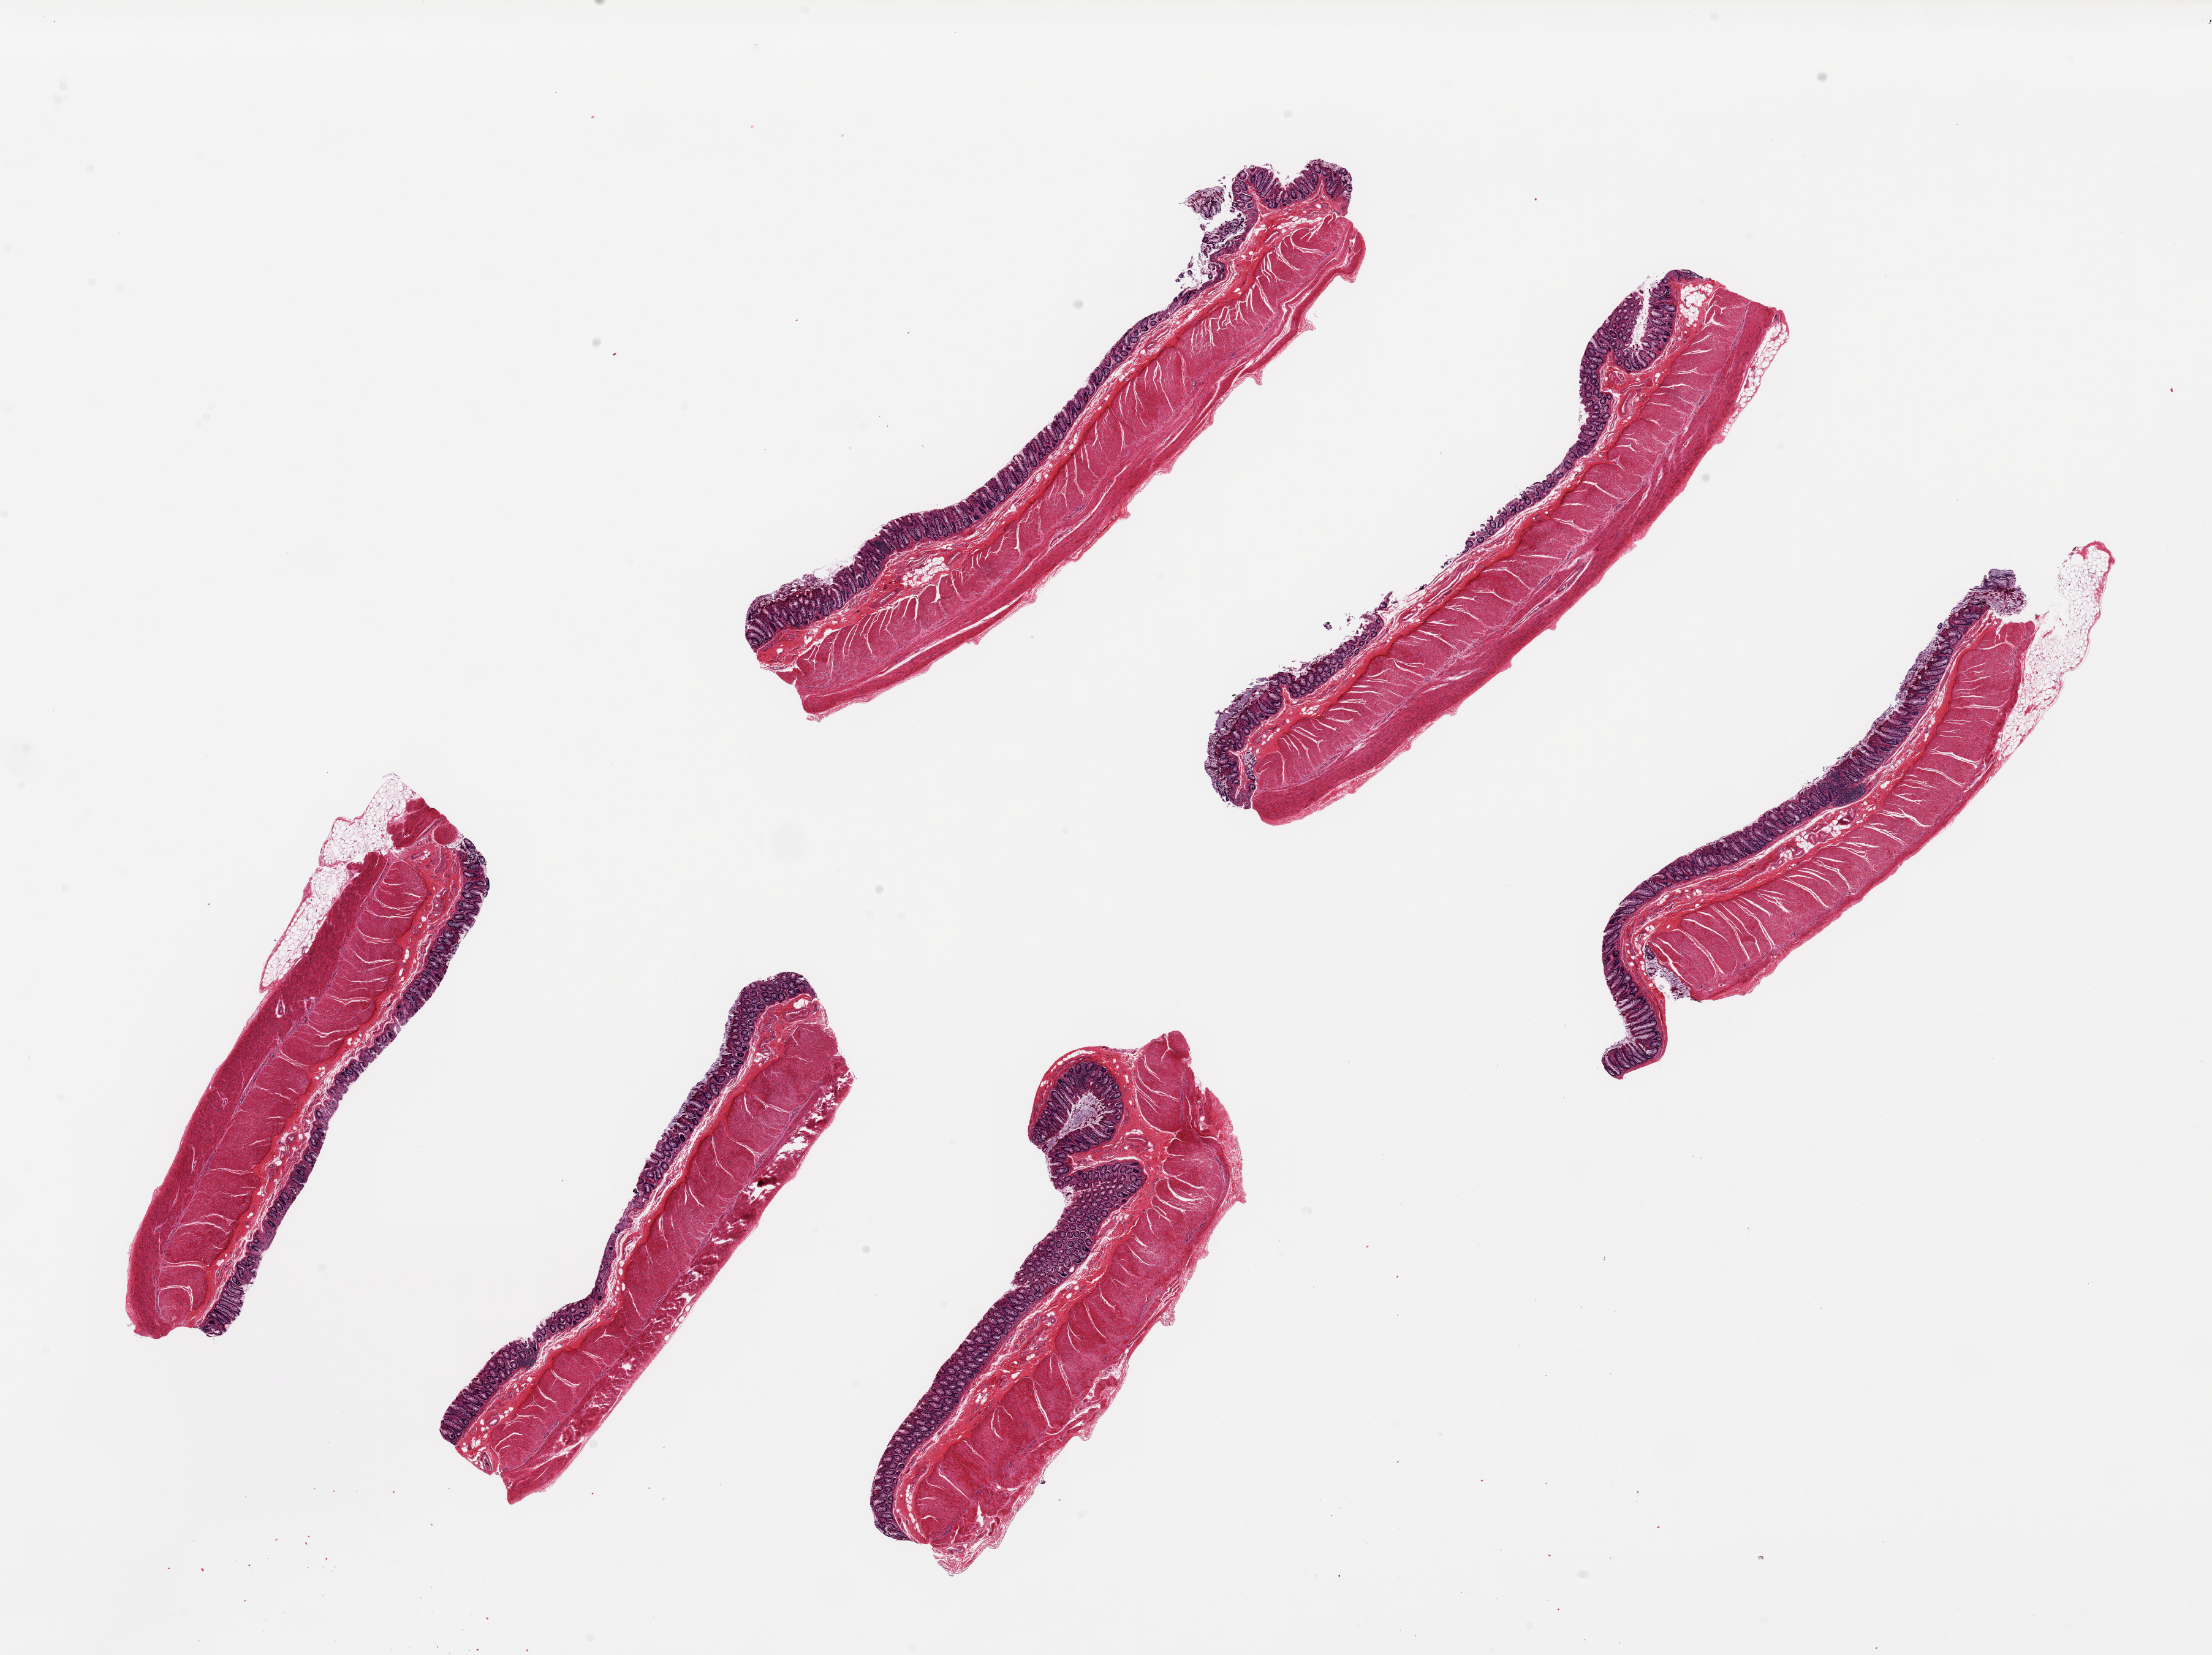
Digitized H&E-stained section, low-resolution overview of the scanned area, about 28.5 x 21.4 mm, PAXgene-fixed paraffin-embedded (PFPE) section, sampled site (target tissue): transverse colon, donor tissue sample. Donor sex: male.
Pathologist's review note for this sample: 6 pieces ~9x1.5mm. Mucosa reasonably well preserved, ~15-20% of thickness.